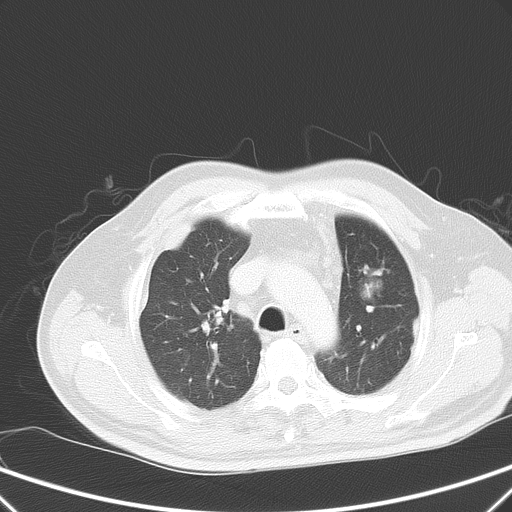
Chest CT, one axial slice; slice 44 of 59 in the series (ordered by position); 120 kVp; lung window (W 1500 / L -600 HU); 5 mm slice thickness; 512 × 512 image matrix. Patient: male, 66 years. Case-level facts recorded for this patient, not image findings: clinical TNM (as recorded): T1c N3 M1a.
Structures marked on this image (bounding box drawn by a radiologist):
- lung tumour (recorded histology: squamous cell carcinoma): bounding box <351,261,394,305> (left, top, right, bottom; pixels)